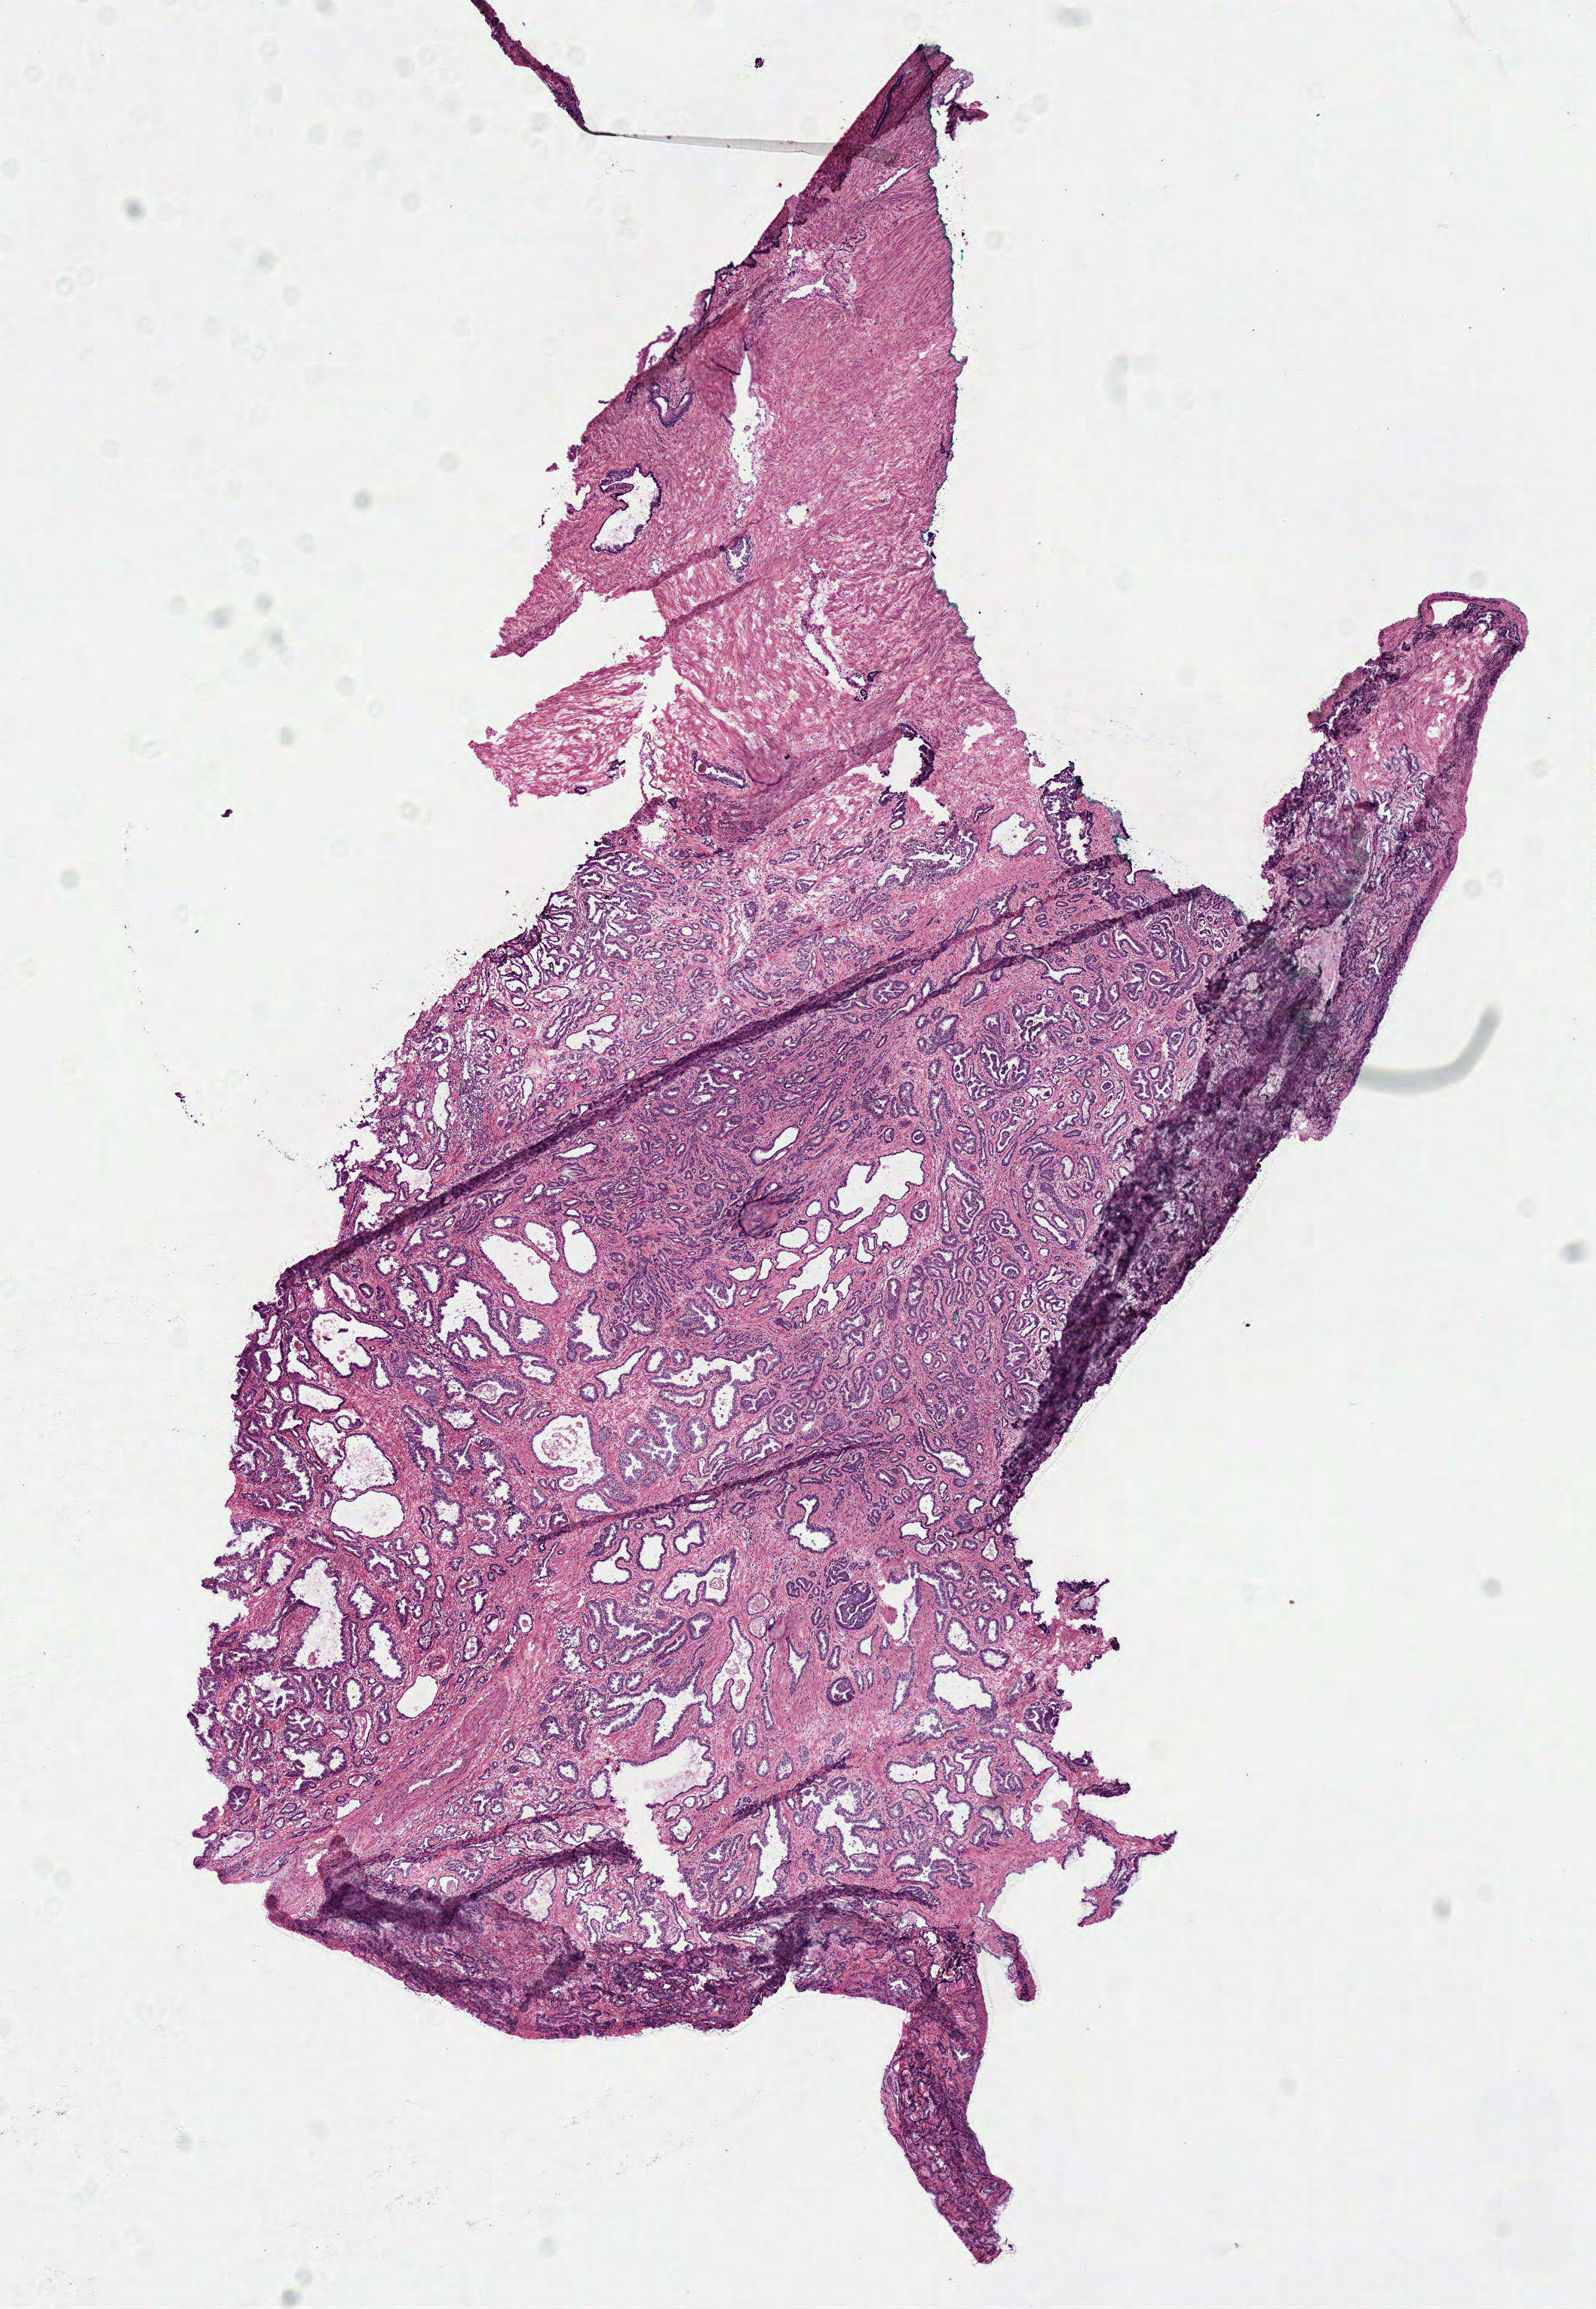
Digitized Hematoxylin and eosin (H&E) stained tissue section (whole slide) — low-resolution overview of the scanned area, about 8.3 x 12.0 mm. Frozen section. Sample: primary tumour, prostate. Male, age 58 years at initial diagnosis. Pathologist review of this section (percent, as recorded): tumour cells 40%, tumour nuclei 60%.
Pathologic diagnosis: Acinar cell carcinoma.